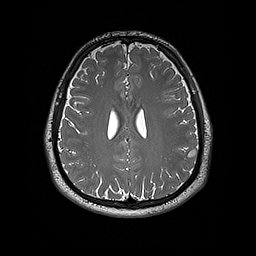
Brain MRI from a brain-tumour surgery series, one axial slice. Position 74 of 192 along the scan axis. 1 mm slice thickness. 256 × 256 image matrix, field of view 250 × 250 mm. Case-level facts recorded for this patient, not image findings: histopathology: Dysembryoplastic neuroepithelial tumor; WHO grade: 1; IDH mutation: no; tumour location: Left Inferior Parietal.
Structures marked on this image (expert manual segmentation):
- tumour: box from (x=187, y=148) to (x=198, y=157) px